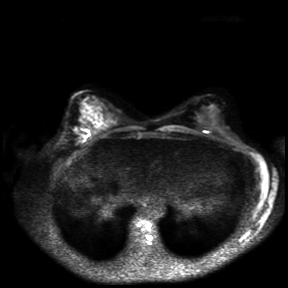
Breast MRI, one axial slice; slice 17 of 30 in the series (ordered by position); diffusion-weighted series; image 2 of 4 stored at this slice position (different b-values; order by instance number); 3 T; 4 mm slice thickness; 288 × 288 image matrix, field of view 360 × 360 mm. Female patient.
Annotated regions visible in this slice (expert manual segmentation):
- tumour on diffusion-weighted imaging: bounding box (x1, y1, x2, y2) in pixels: (73, 129, 90, 138)